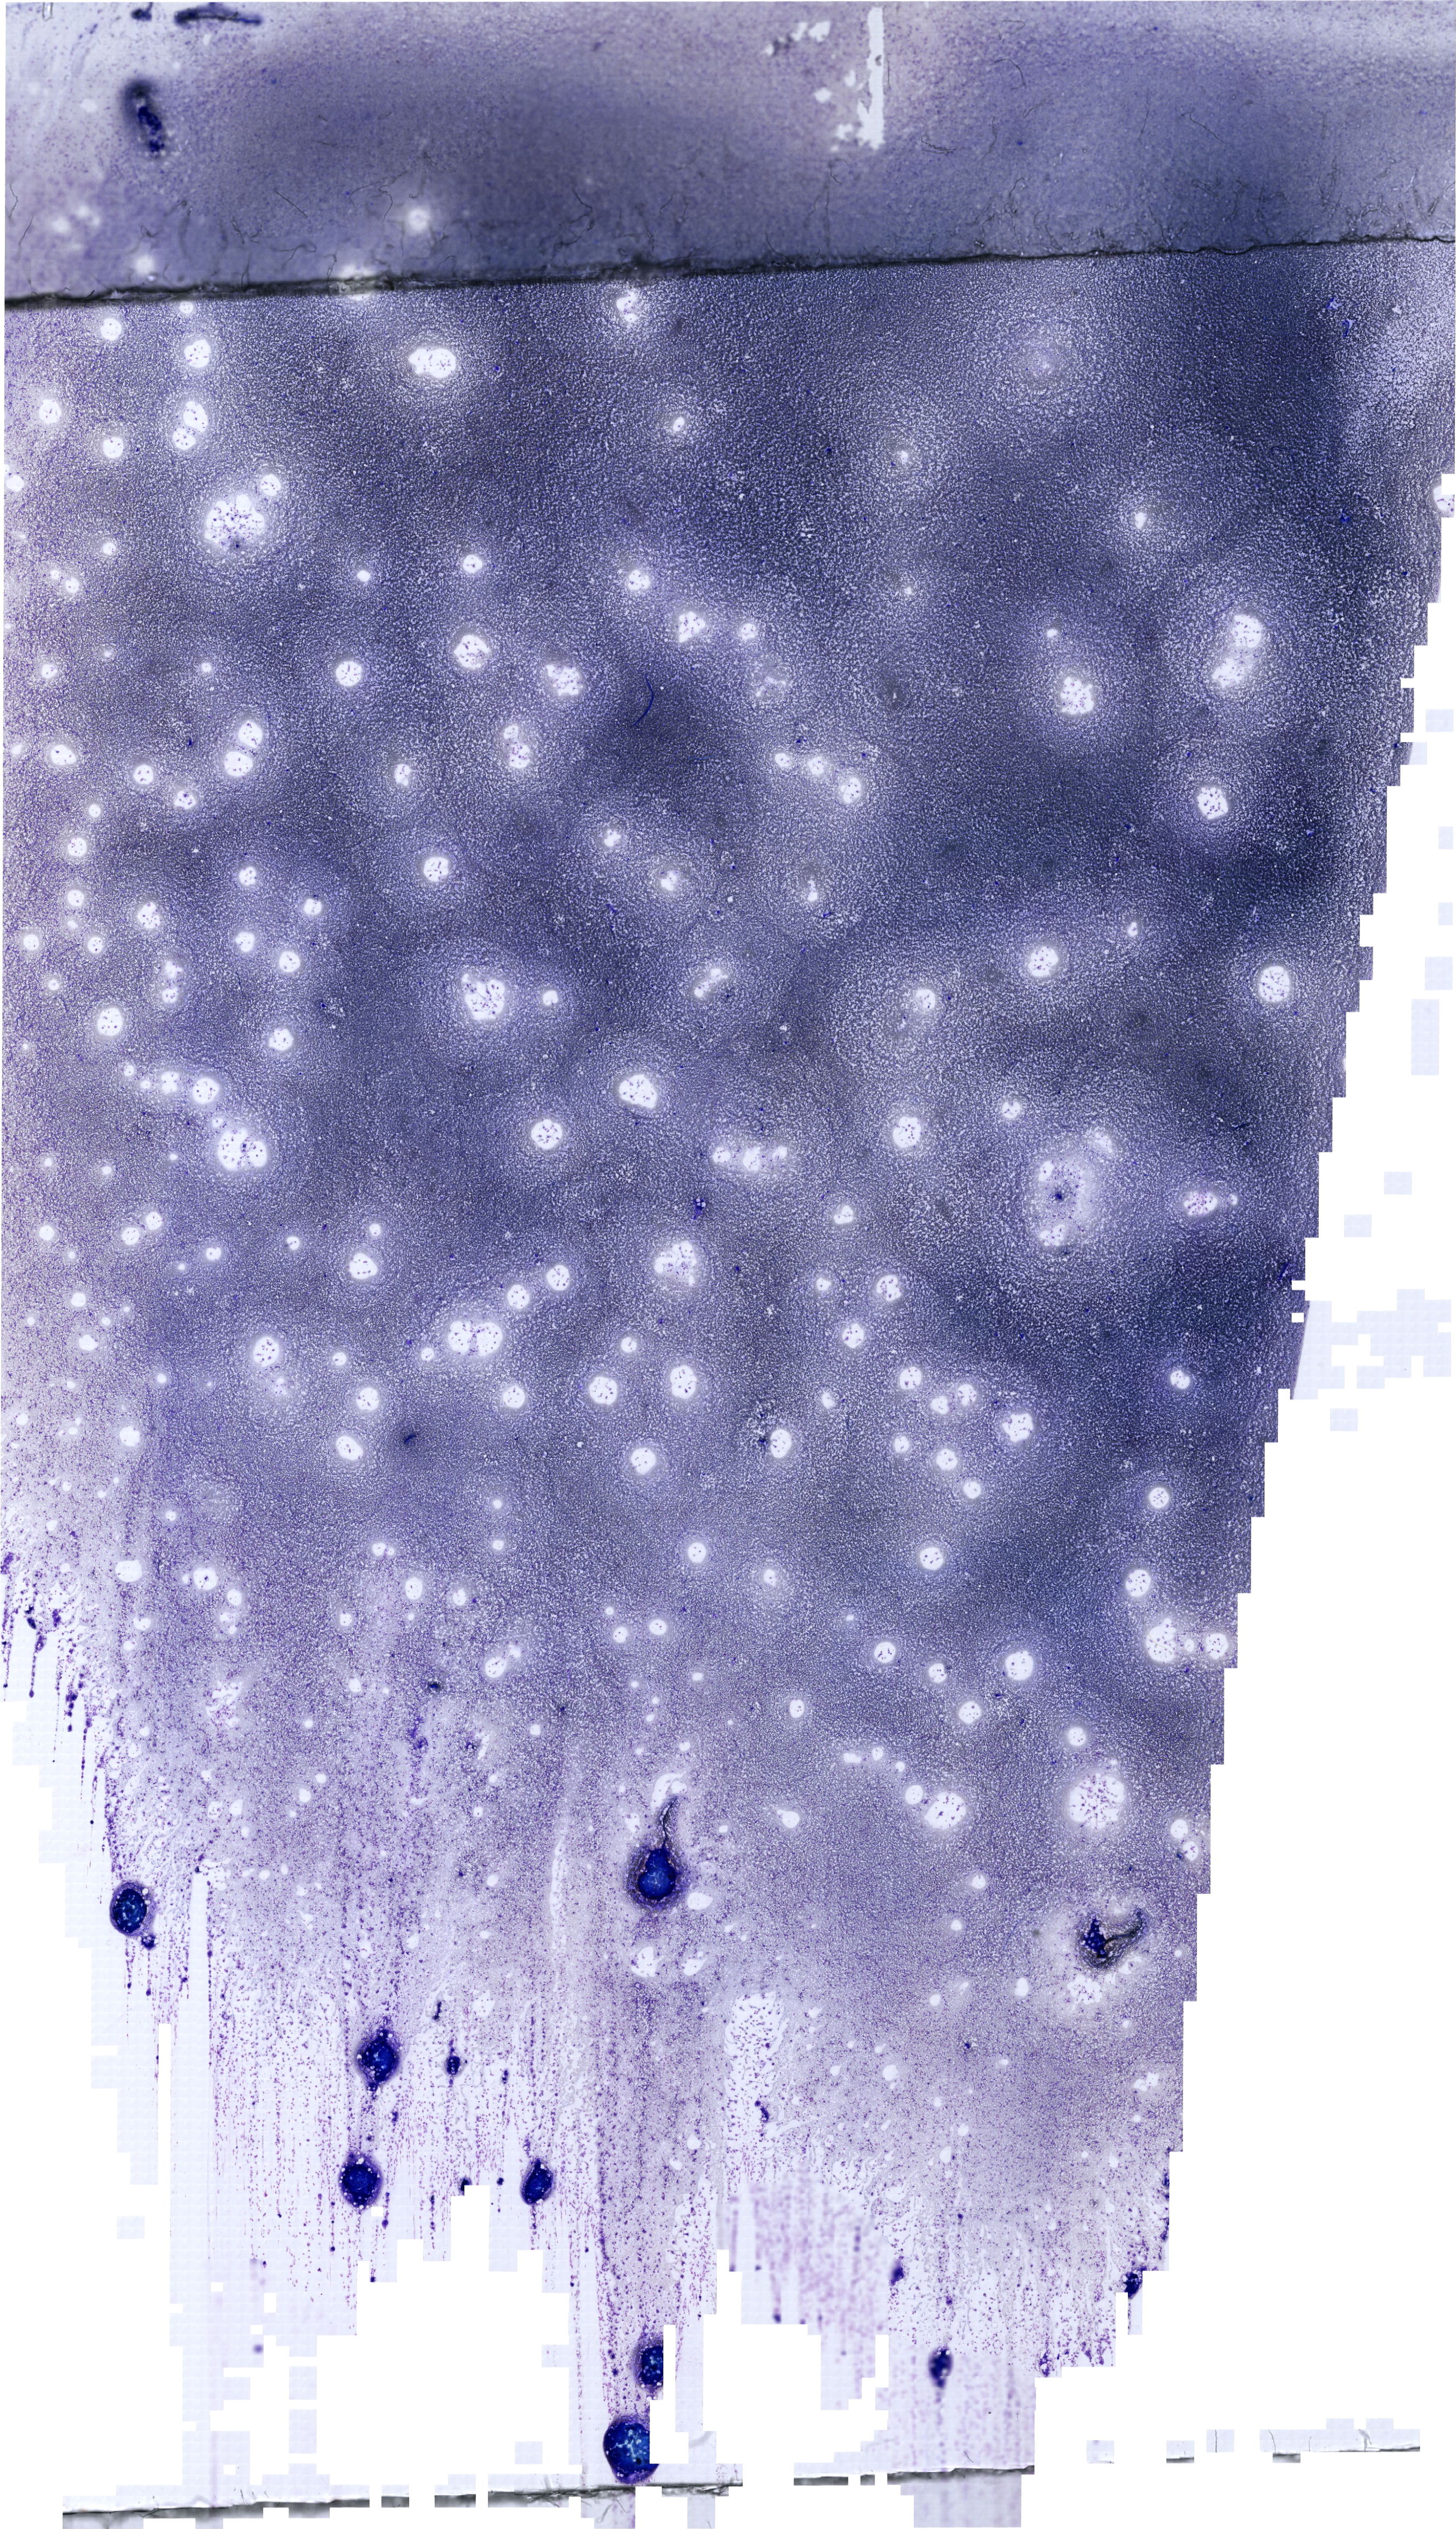
May-Grünwald-Giemsa (MGG)-stained marrow aspirate smear (whole slide), whole scanned area (about 21.2 x 36.8 mm) shown as a low-resolution overview. Patient sex: male.
Diagnosis: Burkitt Leukemia.